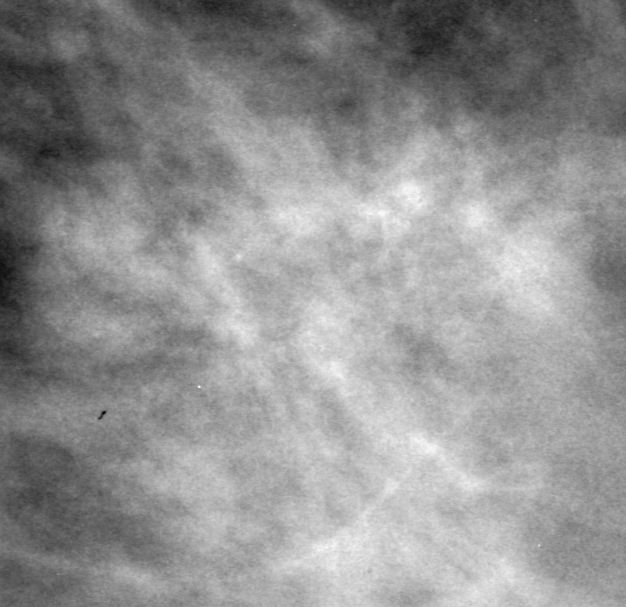
Crop from a digitized film mammogram around one marked abnormality; right breast; MLO view; BI-RADS breast density category 4 (scale 1–4).
- Marked abnormality: mass, shape architectural distortion, margins spiculated; BI-RADS assessment category 4; subtlety rating 4 on a 1 (subtle) to 5 (obvious) scale; pathology (as recorded): benign.